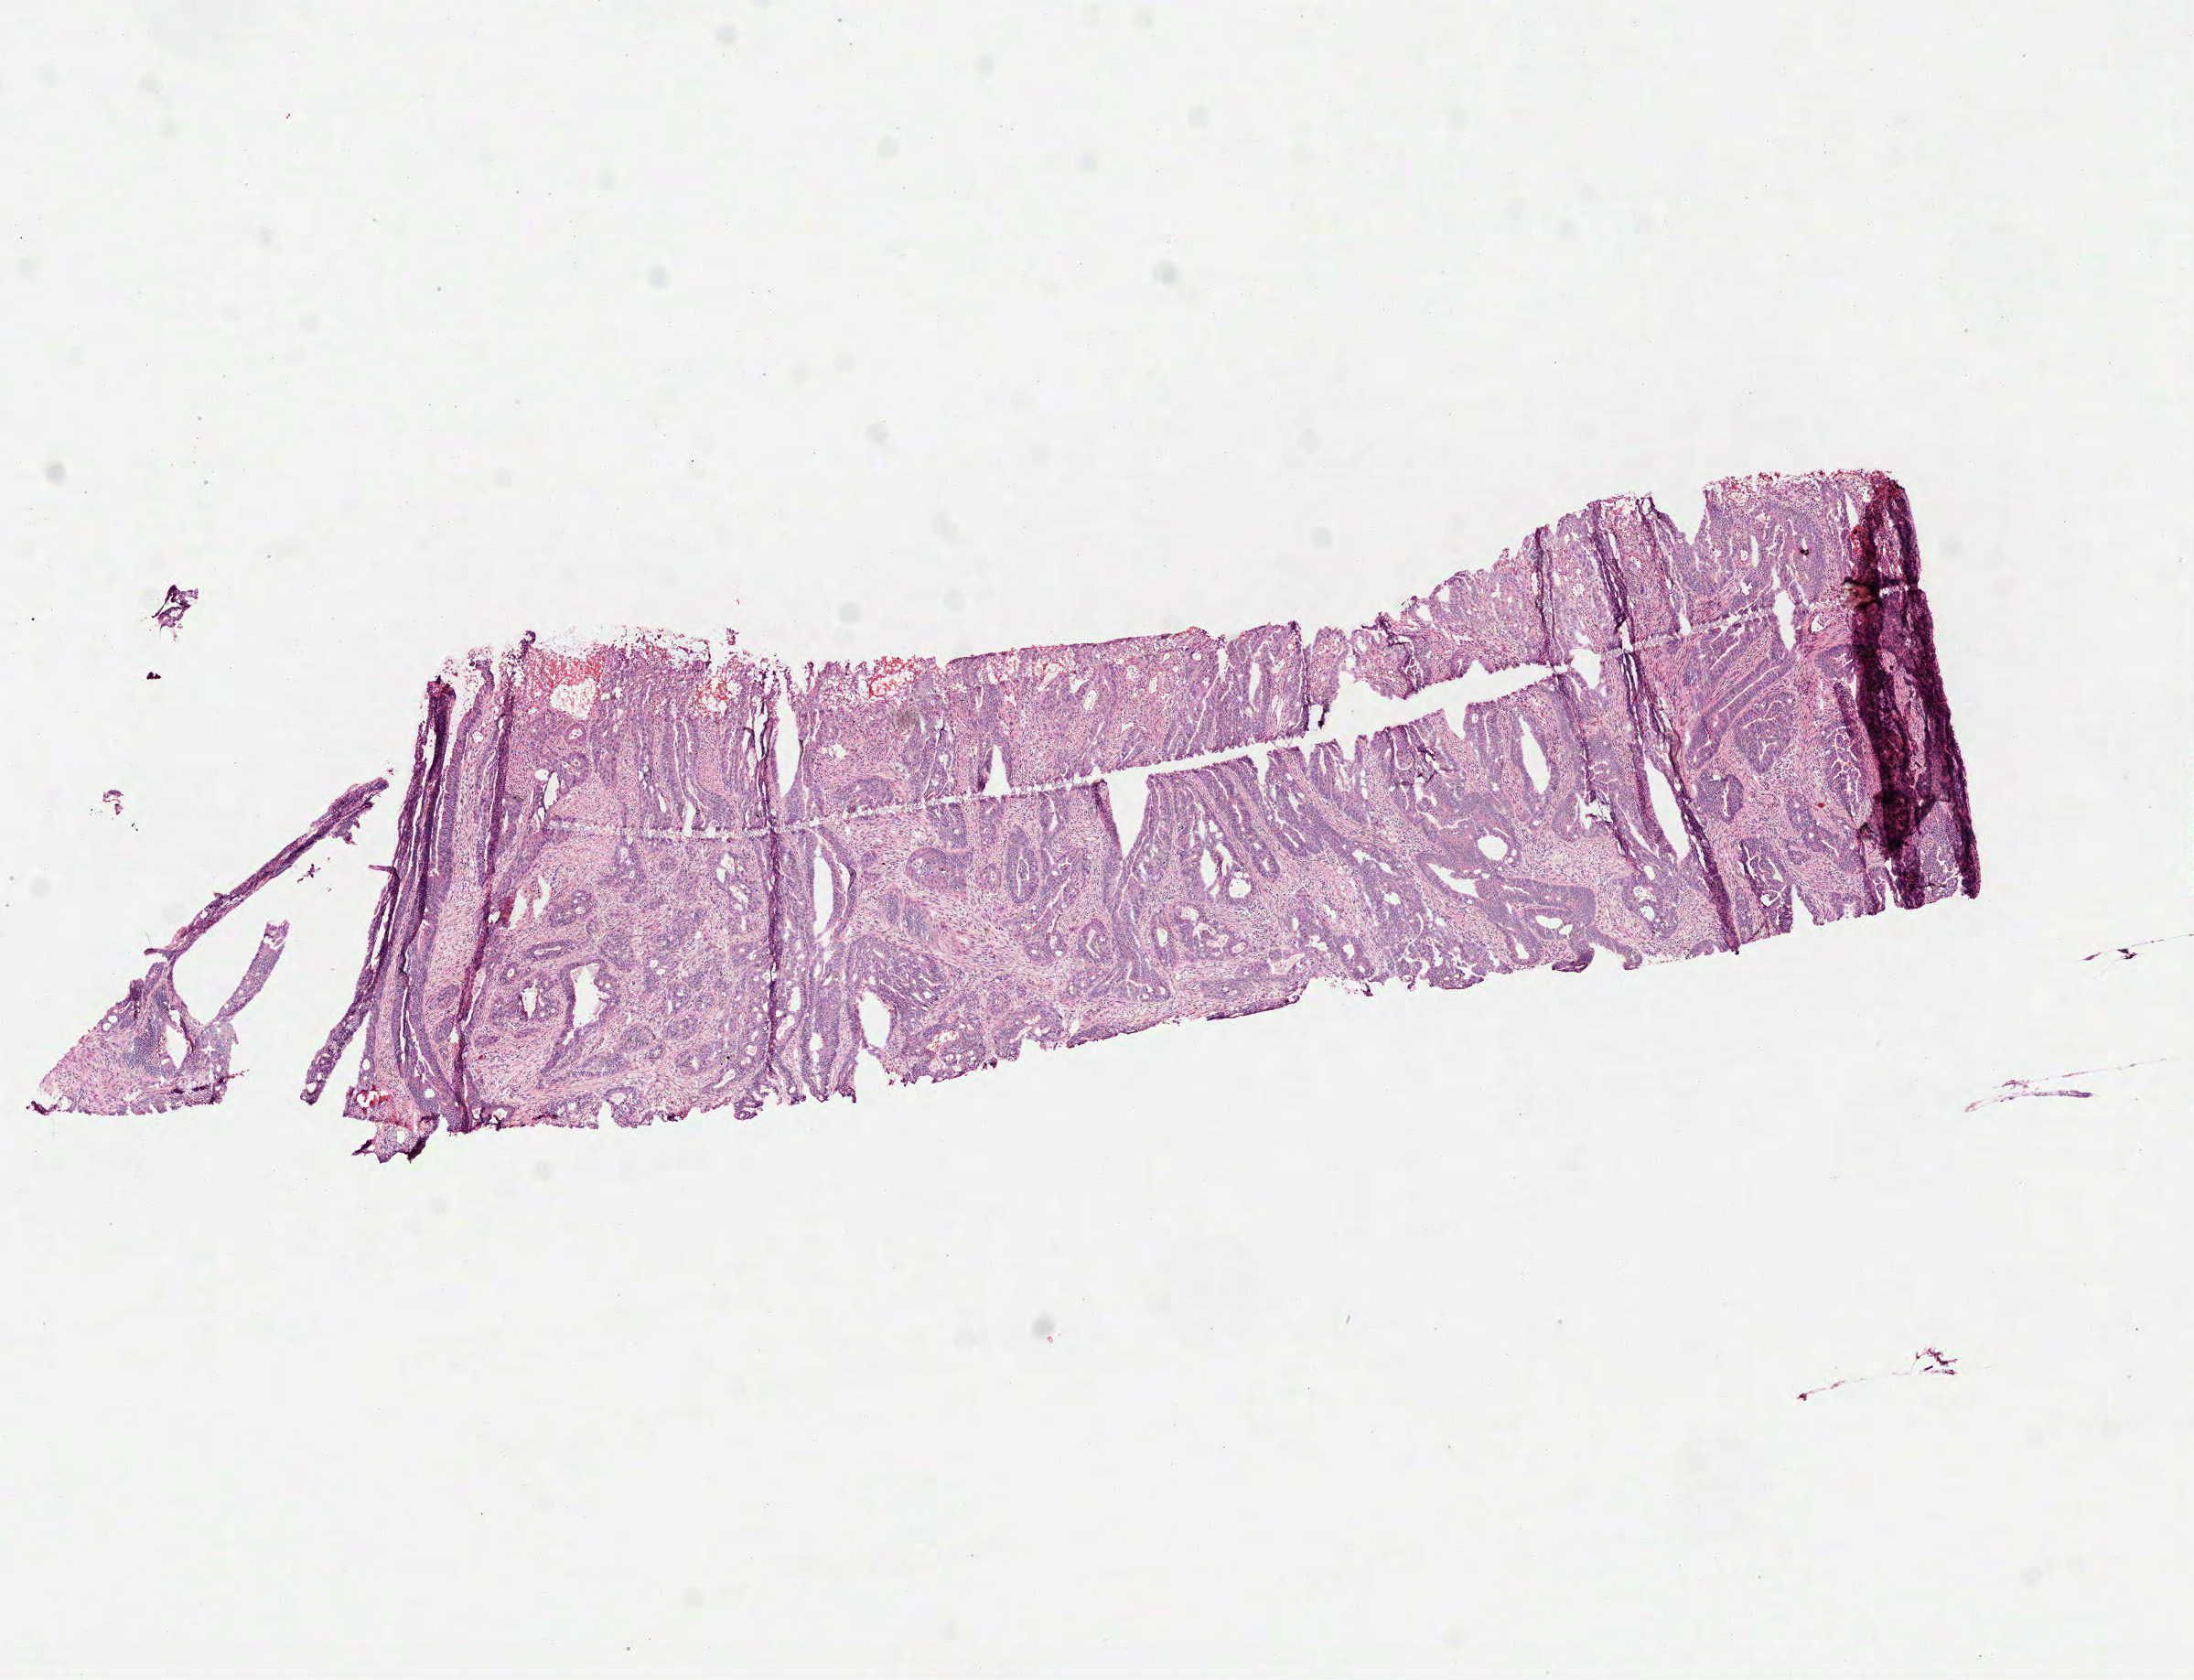
Whole-slide histology image, Hematoxylin and eosin (H&E) stained, whole scanned area (about 9.7 x 7.4 mm, slide scanned at 40x) shown as a low-resolution overview, frozen section from the top of the tissue portion, sample: primary tumour, colon. Patient: male, age at initial diagnosis 57 years. Composition of this section per pathologist review: tumour cells 65%, tumour nuclei 75%, normal cells 0%, stromal cells 34%, necrosis 1%. Infiltration values recorded for this section: lymphocyte infiltration 4%, monocyte infiltration 0%, neutrophil infiltration 1%.
Pathologic diagnosis: Adenocarcinoma, NOS (sigmoid colon). Lymph nodes positive (case pathology): 0 of 11 examined. AJCC pathologic stage: I. TNM: T2 N0 M0.